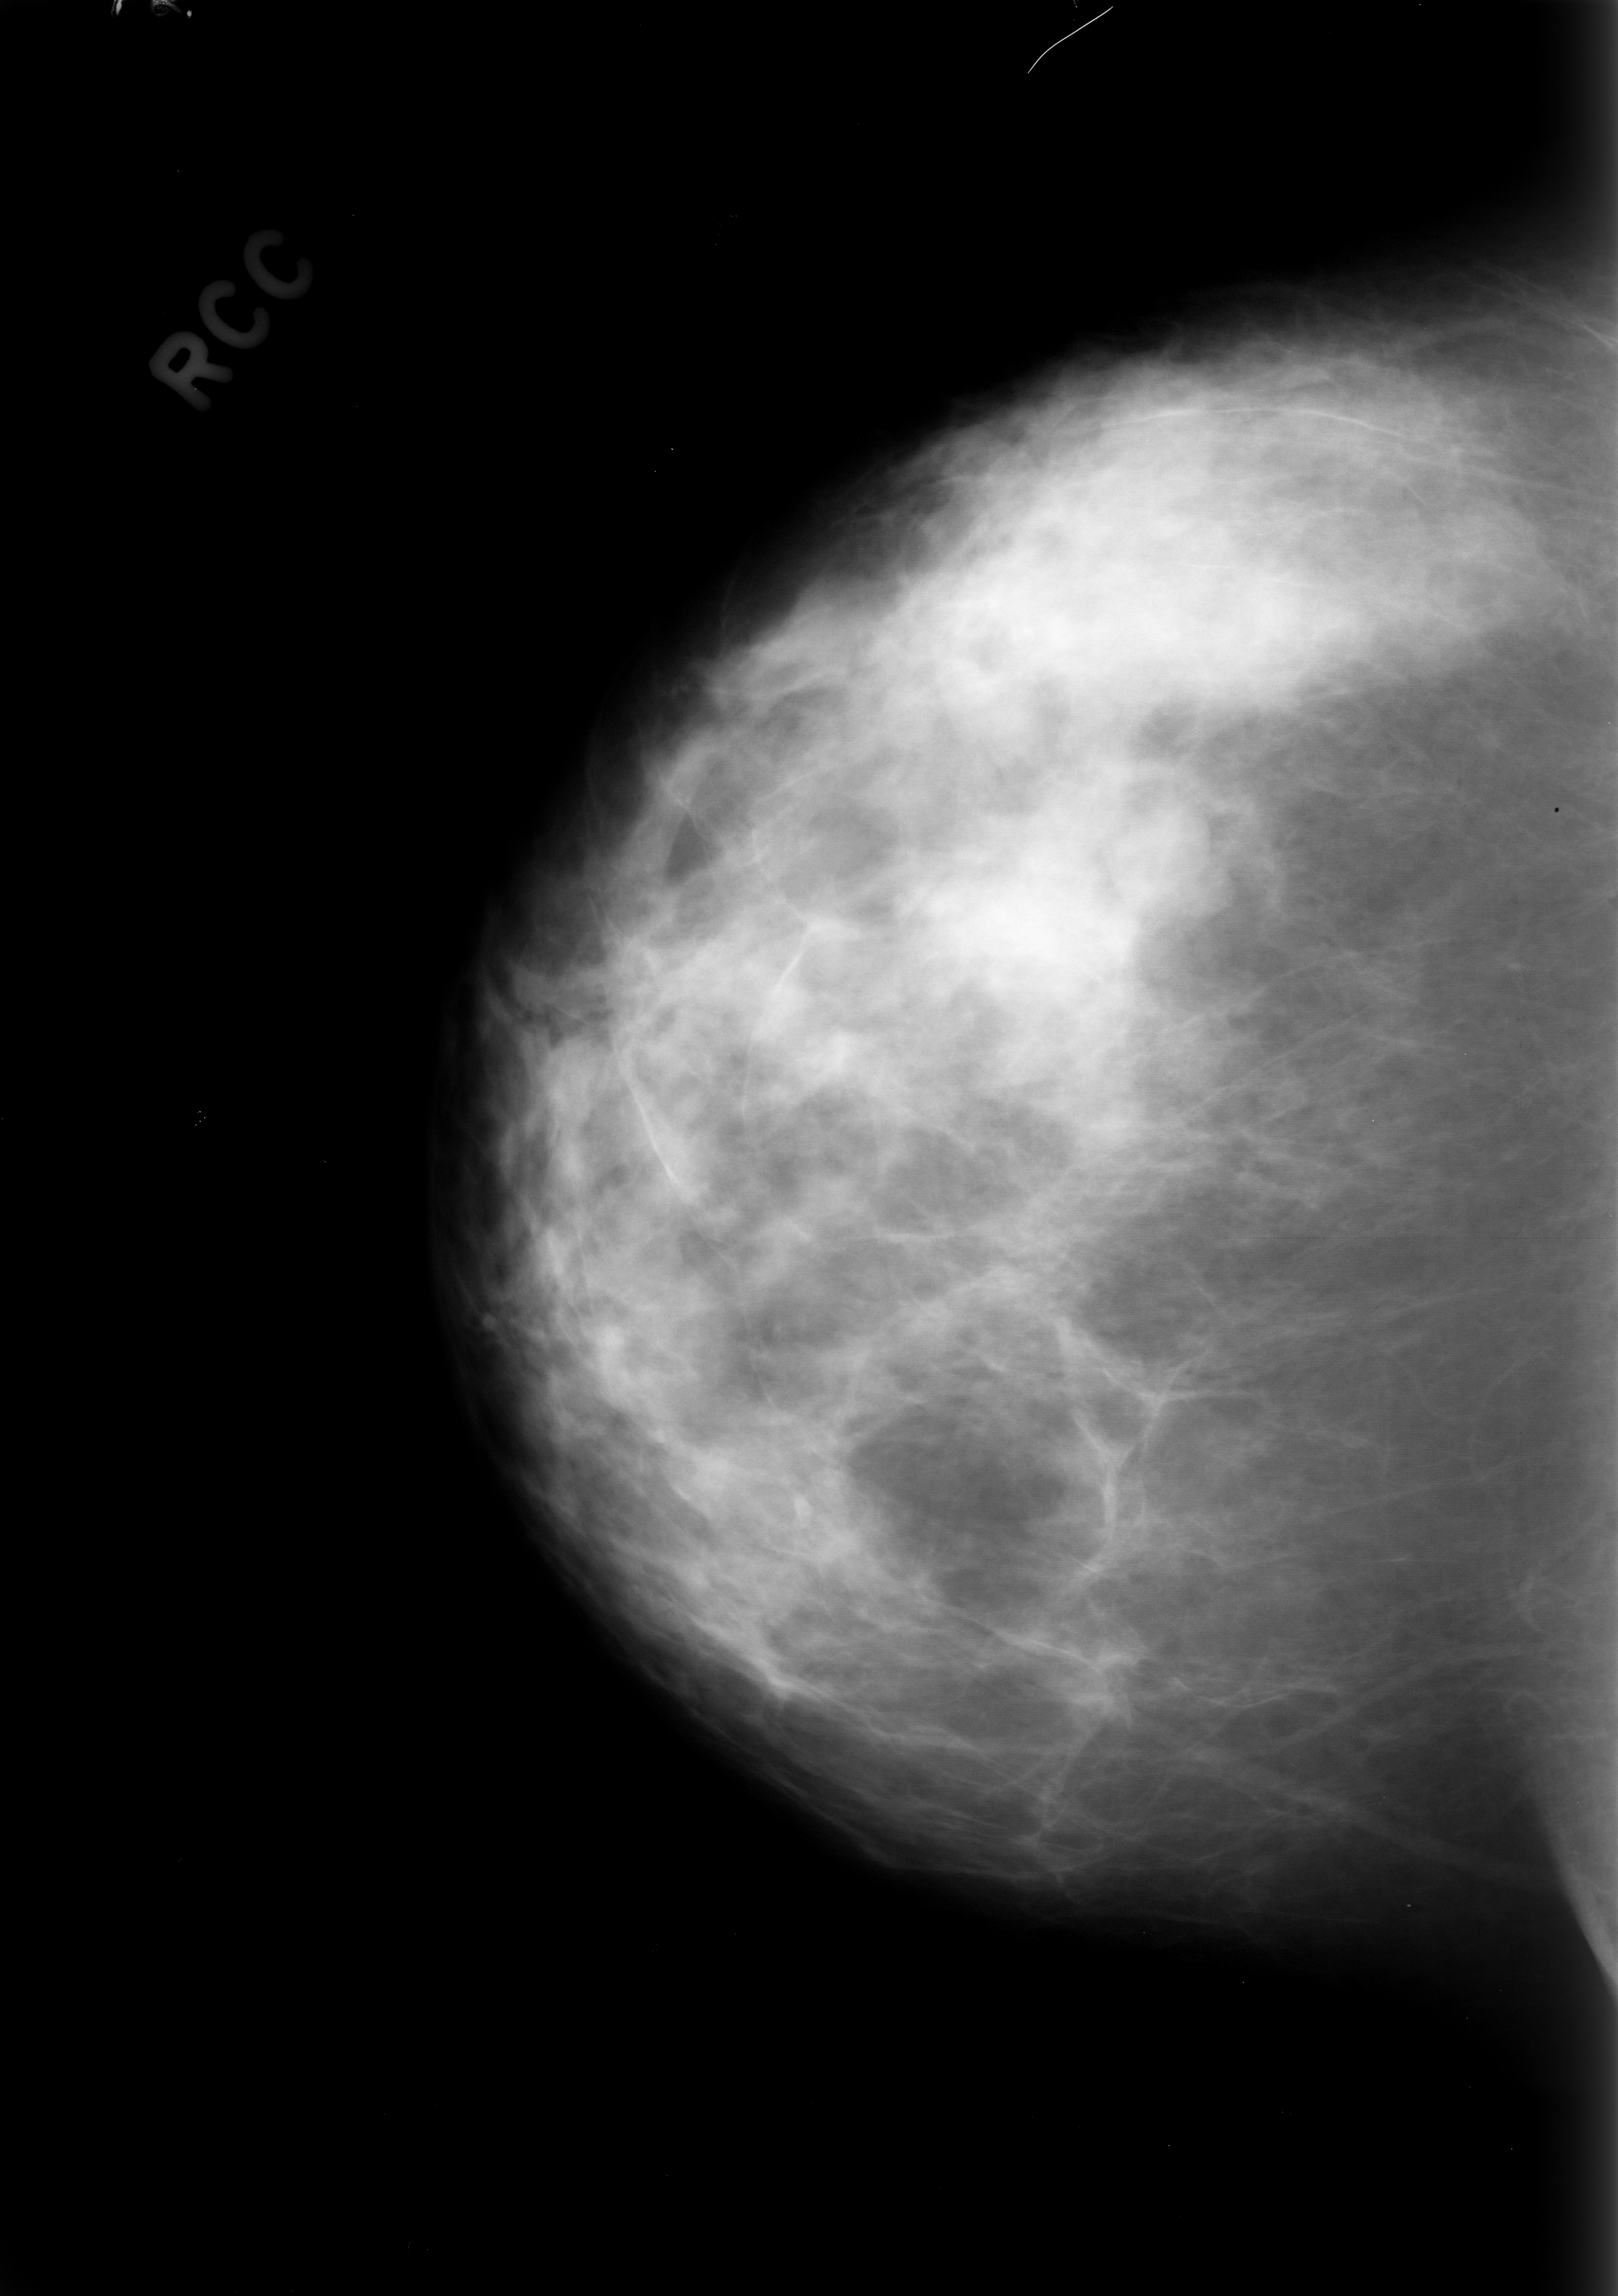
Scanned film-screen mammogram, right breast, CC view, BI-RADS breast density category 2 (scale 1–4).
- Marked abnormality: mass, shape lobulated, margins circumscribed; BI-RADS assessment category 3; subtlety rating 4 on a 1 (subtle) to 5 (obvious) scale; pathology (as recorded): benign.